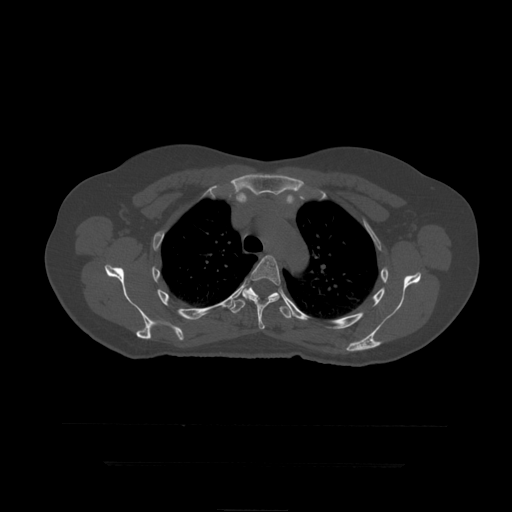
CT including the spine, one axial slice. Position 330 of 399 along the scan axis. Reconstruction kernel STANDARD. Bone window (W 1800 / L 400 HU). 1.25 mm slice thickness. 512 × 512 image matrix, field of view 450 × 450 mm. Patient age 41 years. Case-level facts recorded for this patient, not image findings: primary cancer: breast.
Outlined on this slice (semi-automatic segmentation, software-assisted and operator-edited):
- T5 vertebra: box from (x=242, y=255) to (x=281, y=330) px
- T6 vertebra: (x=231, y=283)–(x=293, y=319)